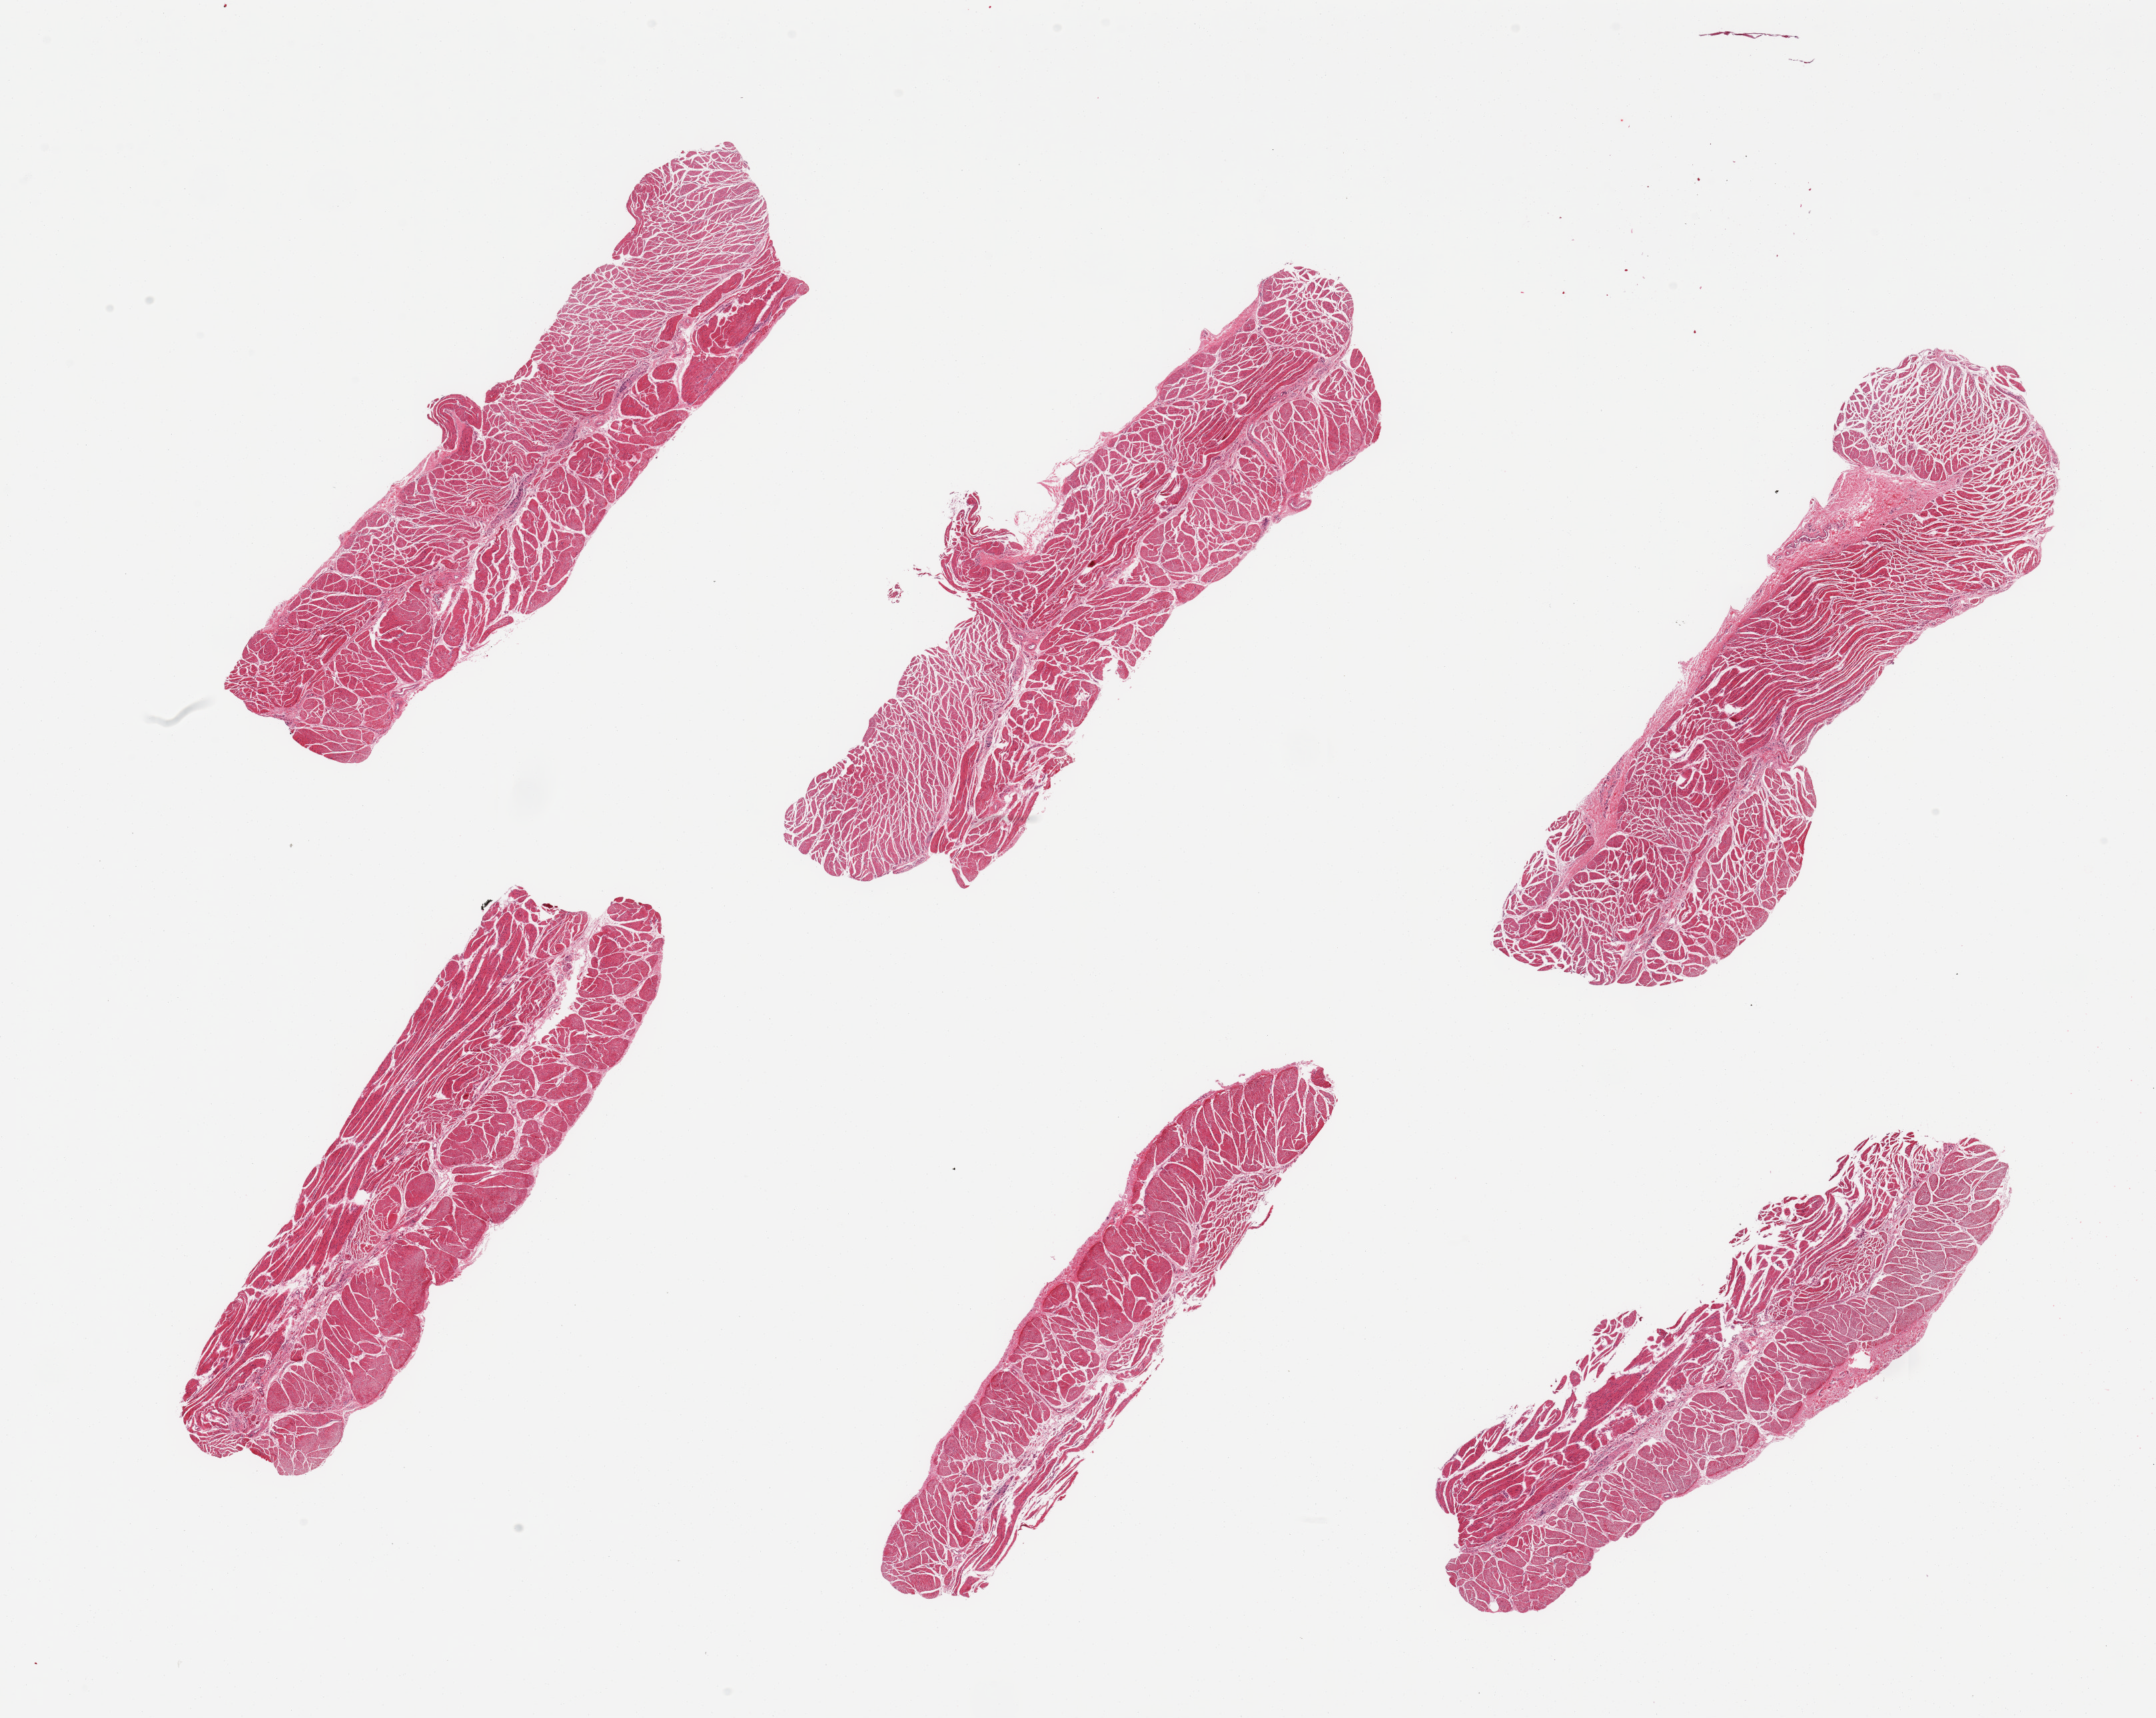
Whole-slide image, haematoxylin and eosin stain, shown as a low-resolution overview of the whole scanned area (about 25.6 x 20.4 mm). PAXgene-fixed, paraffin-embedded tissue. Target tissue: esophageal muscle. Tissue donor sample. Donor sex: male.
• pathologist's review note for this sample: 6 pieces; target muscularis